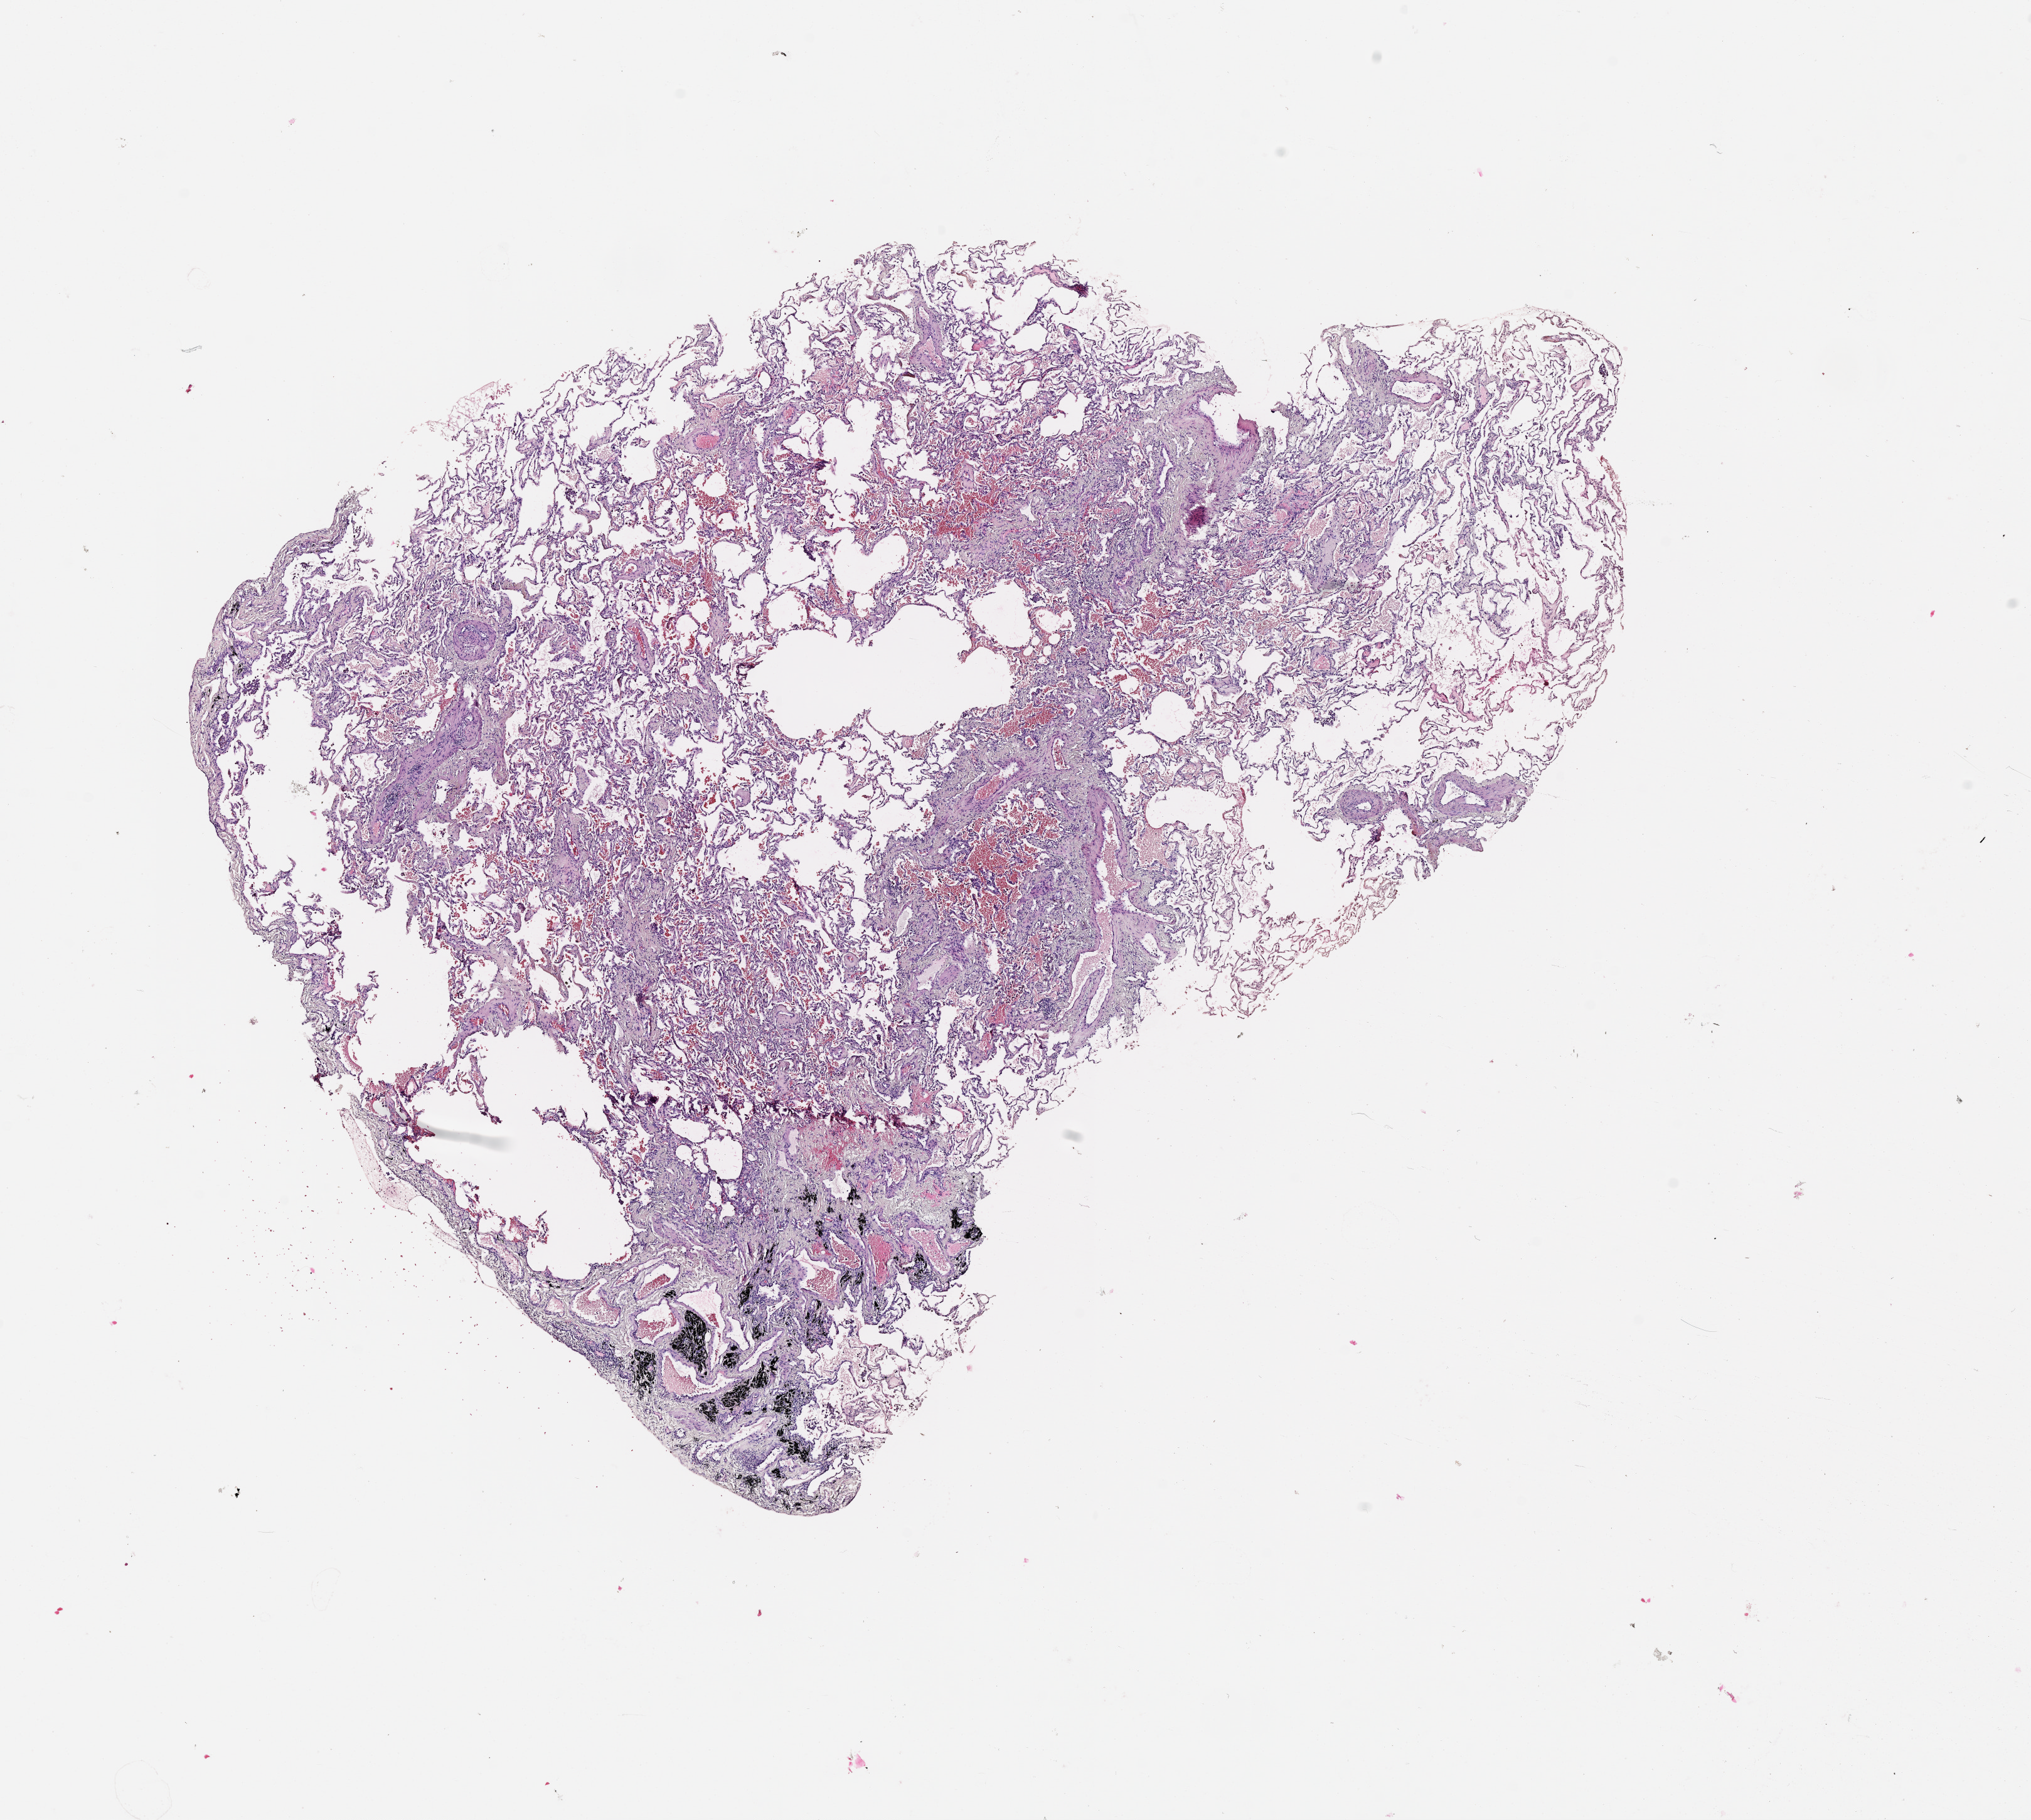
Digitized H&E tissue section (whole slide), low-resolution overview of the scanned area, about 13.0 x 11.7 mm (acquisition: 20x scan), lung, normal (non-tumour) tissue. Male, 68 y/o.
This section: normal (non-tumour) tissue from the same patient. Patient diagnosis: Adenocarcinoma, NOS.